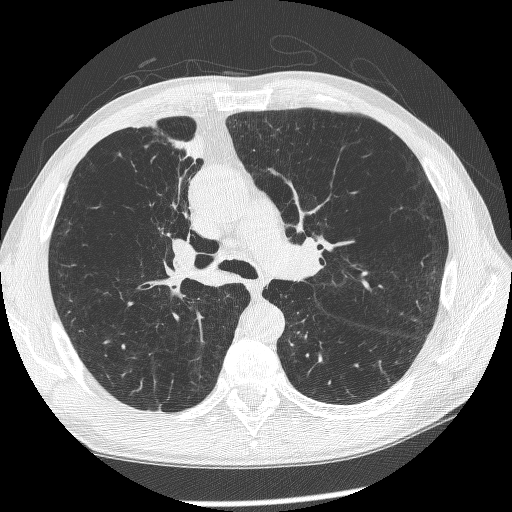
Low-dose screening chest CT, axial slice; first (baseline) screen; lung window (W 1500 / L -600 HU); 512 × 512 image matrix. Male, age 60 years at enrolment.
Lesion marked by an expert reader, bounding box [x1, y1, x2, y2] px = [144, 206, 224, 298]. The exam's reader record, not a measurement of the box and not confirmed to be the same lesion: non-calcified nodule or mass ≥4 mm, right upper lobe, 12 × 8 mm, spiculated (stellate) margins, mixed attenuation. Lung cancer was diagnosed 208 days after this screen: squamous cell carcinoma, NOS, right upper lobe, right middle lobe, right main stem bronchus, poorly differentiated (G3), stage IV (AJCC 6th edition).